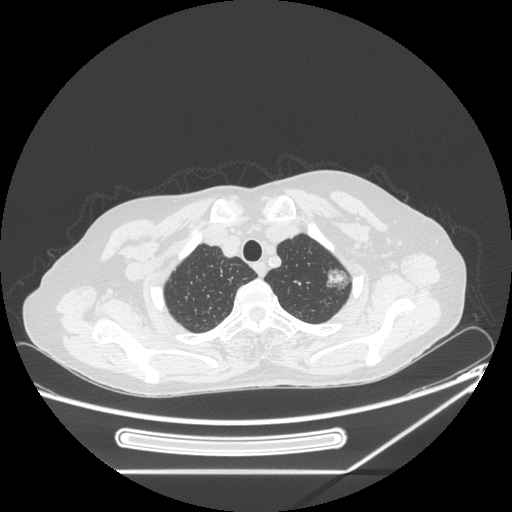
Chest CT, one axial slice; position 210 of 250 along the scan axis; 120 kVp; lung window (W 1500 / L -600 HU); 1.25 mm slice thickness; 512 × 512 image matrix. Patient: female, 57 years. From the clinical record (not read from this slice): clinical TNM (as recorded): T1c N0 M0.
Annotated regions visible in this slice (rectangle marked by the reading radiologist):
- lung tumour (recorded histology: adenocarcinoma): box from (x=321, y=262) to (x=351, y=295) px